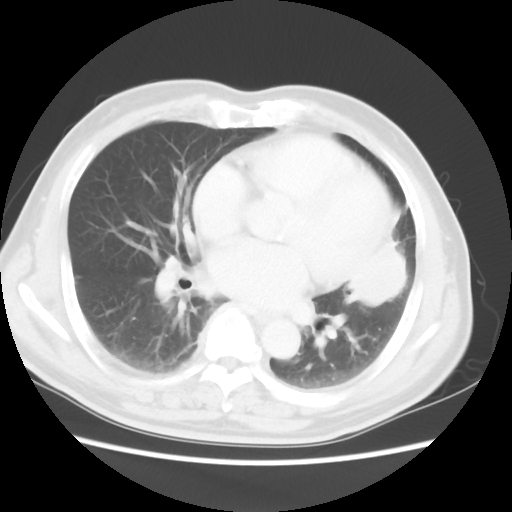
Chest CT, one axial slice; slice 22 of 50 in the series (ordered by position); reconstruction kernel STANDARD; 120 kVp; lung window (W 1500 / L -600 HU); 5 mm slice thickness; 512 × 512 image matrix, field of view 360 × 360 mm. Patient: male, 69 years. Case-level facts recorded for this patient, not image findings: clinical TNM (as recorded): T3 N1 M1a.
Outlined on this slice (bounding box drawn by a radiologist):
- lung tumour (recorded histology: squamous cell carcinoma): box from (x=341, y=237) to (x=417, y=315) px